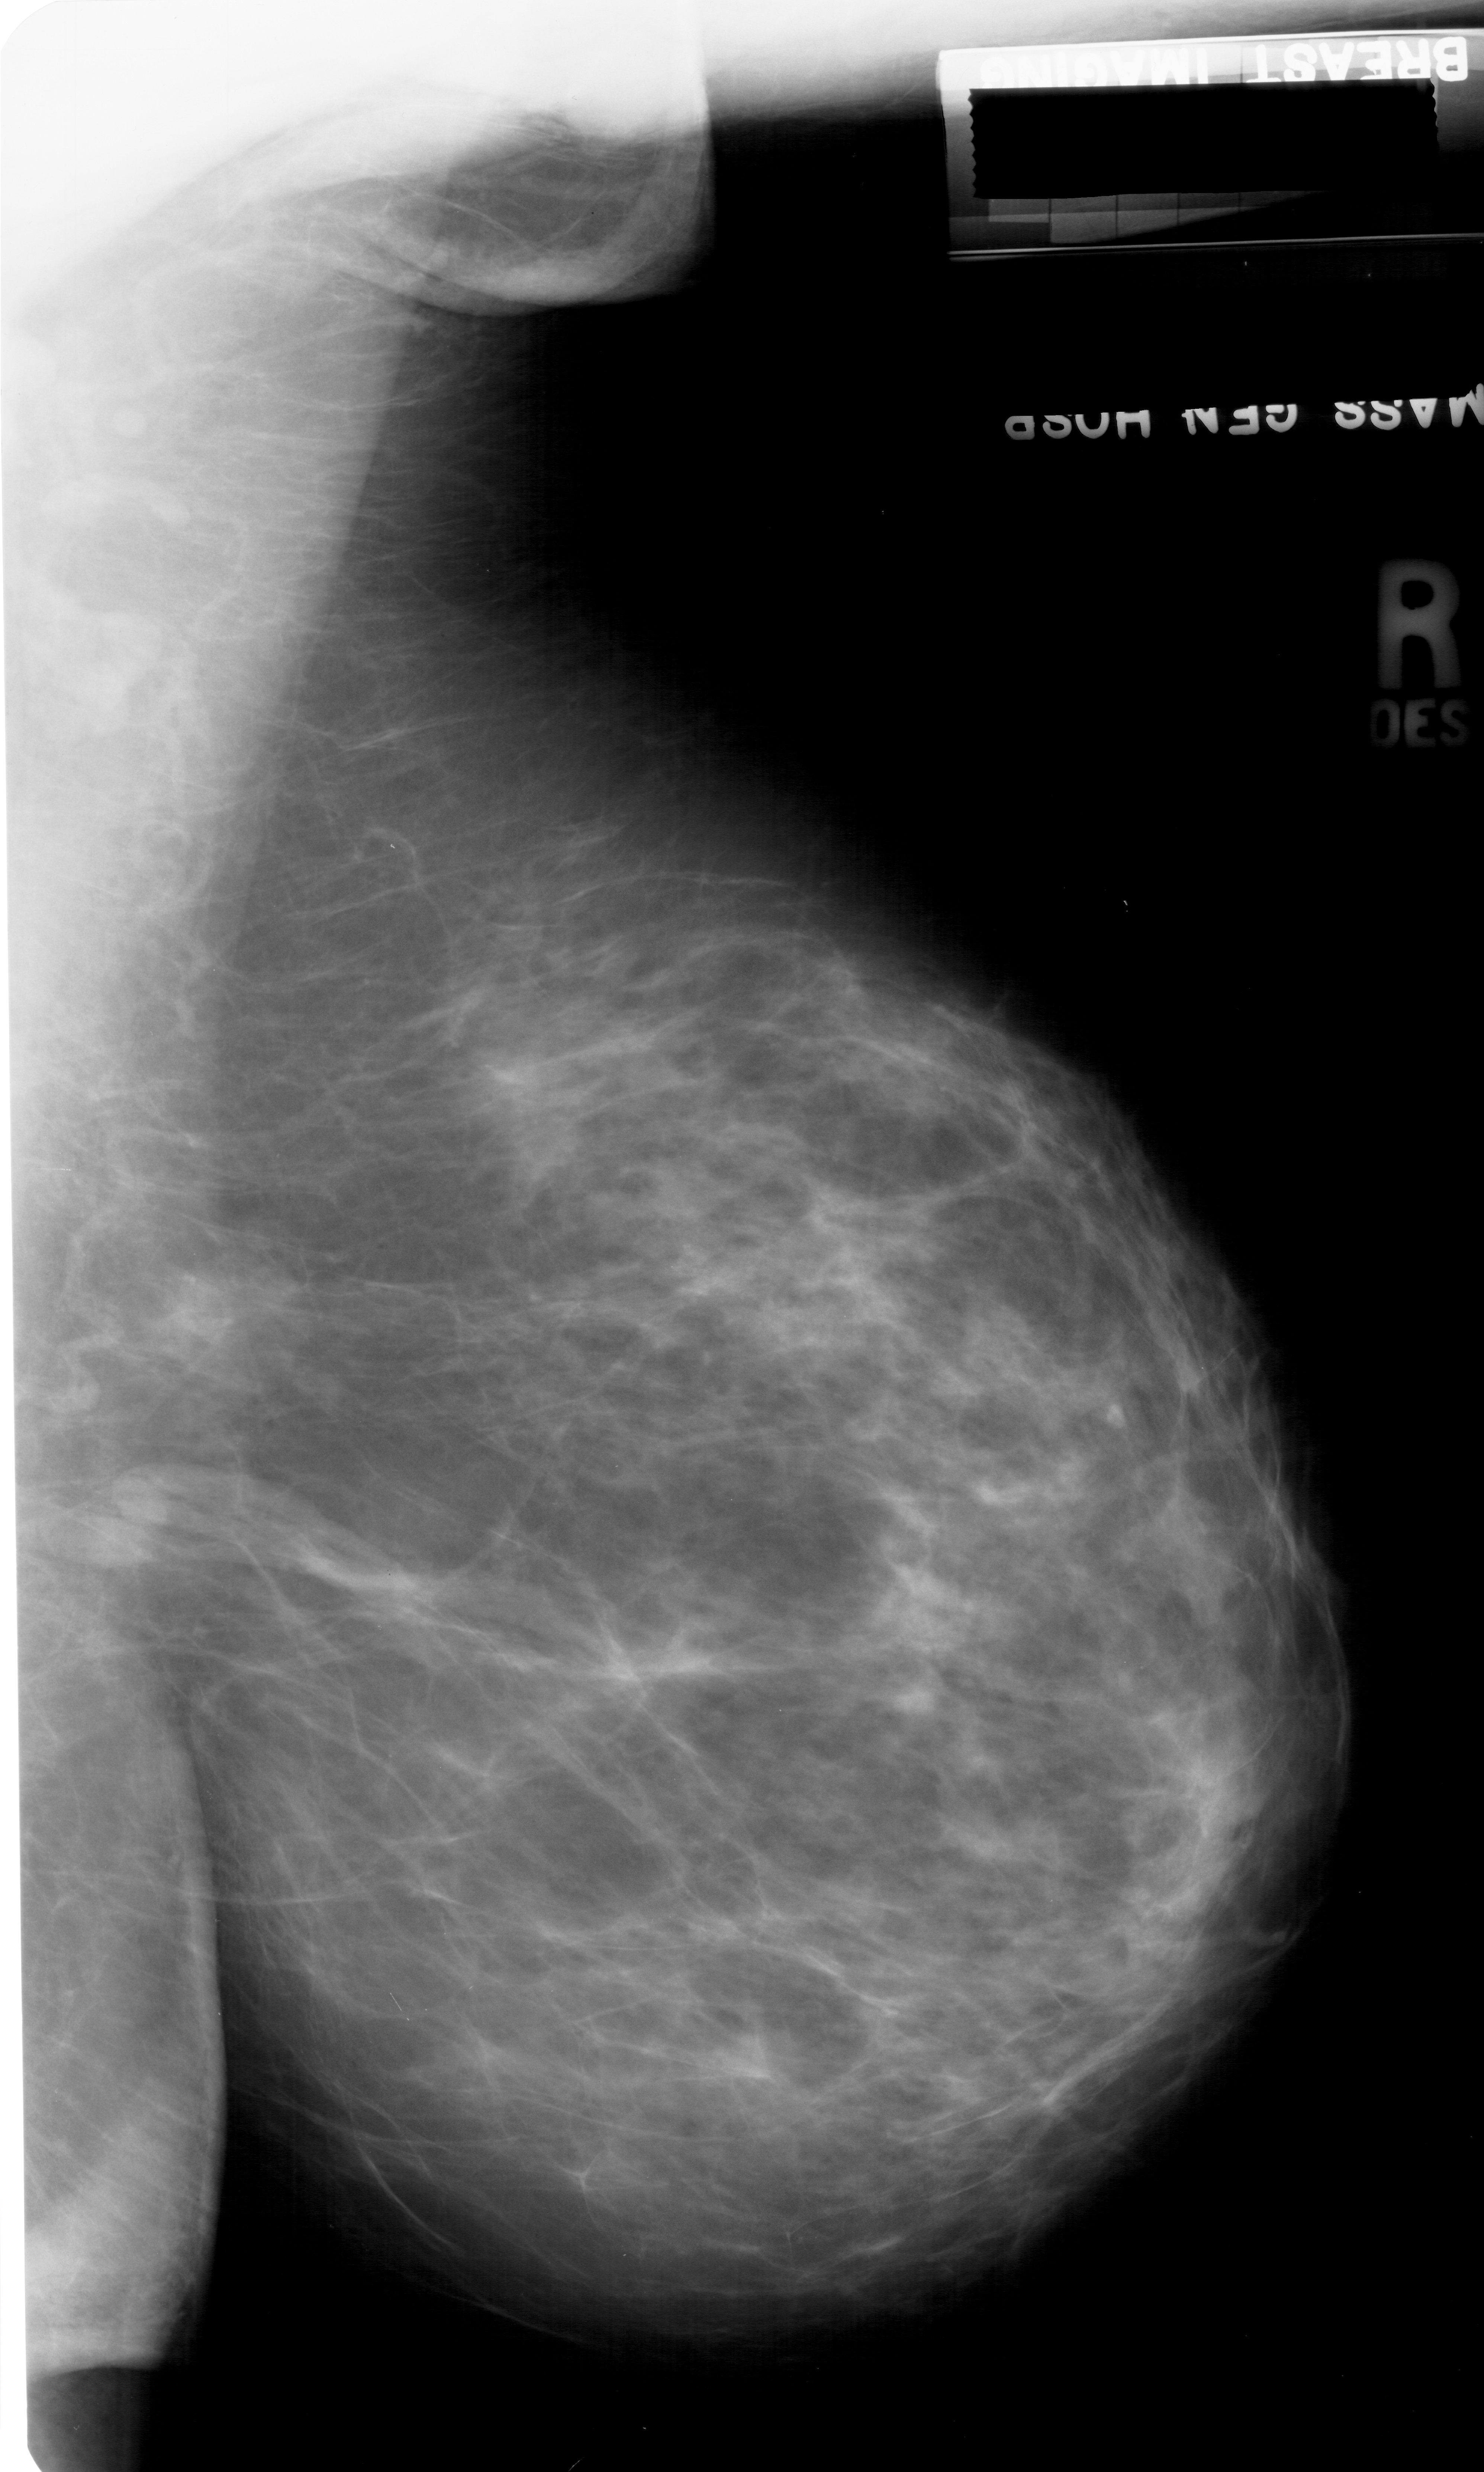
Digitized screen-film mammogram; right breast; mediolateral oblique (MLO) view; breast composition: heterogeneously dense (BI-RADS density category 3 of 4).
Abnormality record for this image: mass, shape irregular, margins ill defined; BI-RADS assessment category 4; subtlety rating 2 on a 1 (subtle) to 5 (obvious) scale; pathology result (as recorded, not read from the image): benign.